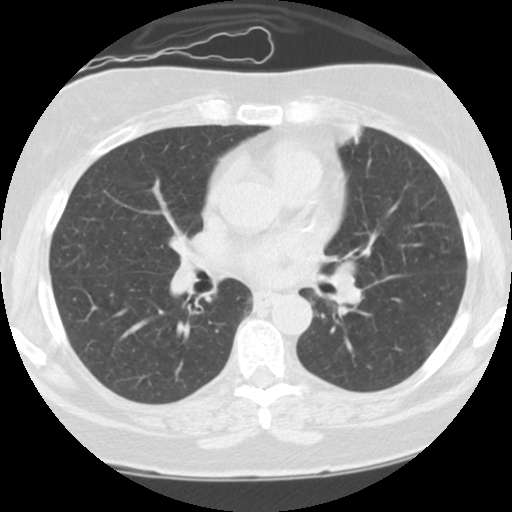
Low-dose screening chest CT, one axial slice. Position 59 of 108 along the scan axis. Reconstruction kernel STANDARD. 120 kVp. Lung window (W 1500 / L -600 HU). 2.5 mm slice thickness. 512 × 512 image matrix, field of view 300 × 300 mm.
Structures marked on this image (expert manual segmentation):
- lesion 1 (tumor, hilum of left lung): bounding box [x1, y1, x2, y2] px = [330, 256, 361, 310]